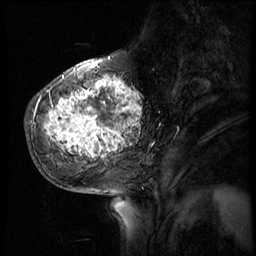
Breast MRI (dynamic contrast-enhanced), one sagittal slice; position 20 of 56 along the scan axis; 4 images stored at this slice position (order not interpretable as contrast timing); 1.5 T; TE 4.2 ms, TR 8.9 ms; 256 × 256 image matrix, field of view 220 × 220 mm. Patient: female, 51 years. Case-level facts recorded for this patient, not image findings: setting: breast cancer imaged before/during neoadjuvant chemotherapy; receptor status: triple-negative.
Annotated regions visible in this slice (semi-automatic segmentation, software-assisted and operator-edited):
- analysis volume of interest (the breast-tissue region the enhancement analysis was run in; not a lesion): bounding box <30,70,150,173> (left, top, right, bottom; pixels)
- tumour enhancement mask (voxels above the 140 % enhancement threshold inside the analysis volume of interest): <36,76,142,159>